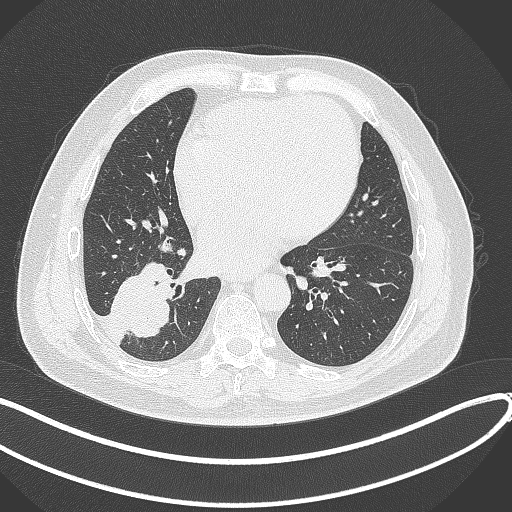
Chest CT, one axial slice. Slice 143 of 360 in the series (ordered by position). Reconstruction kernel B70f. Lung window (W 1500 / L -600 HU). 1 mm slice thickness. 512 × 512 image matrix, field of view 400 × 400 mm. Patient: male, 59 years.
Annotated regions visible in this slice (bounding box drawn by a radiologist):
- lung tumour (recorded histology: adenocarcinoma): box from (x=107, y=251) to (x=174, y=342) px